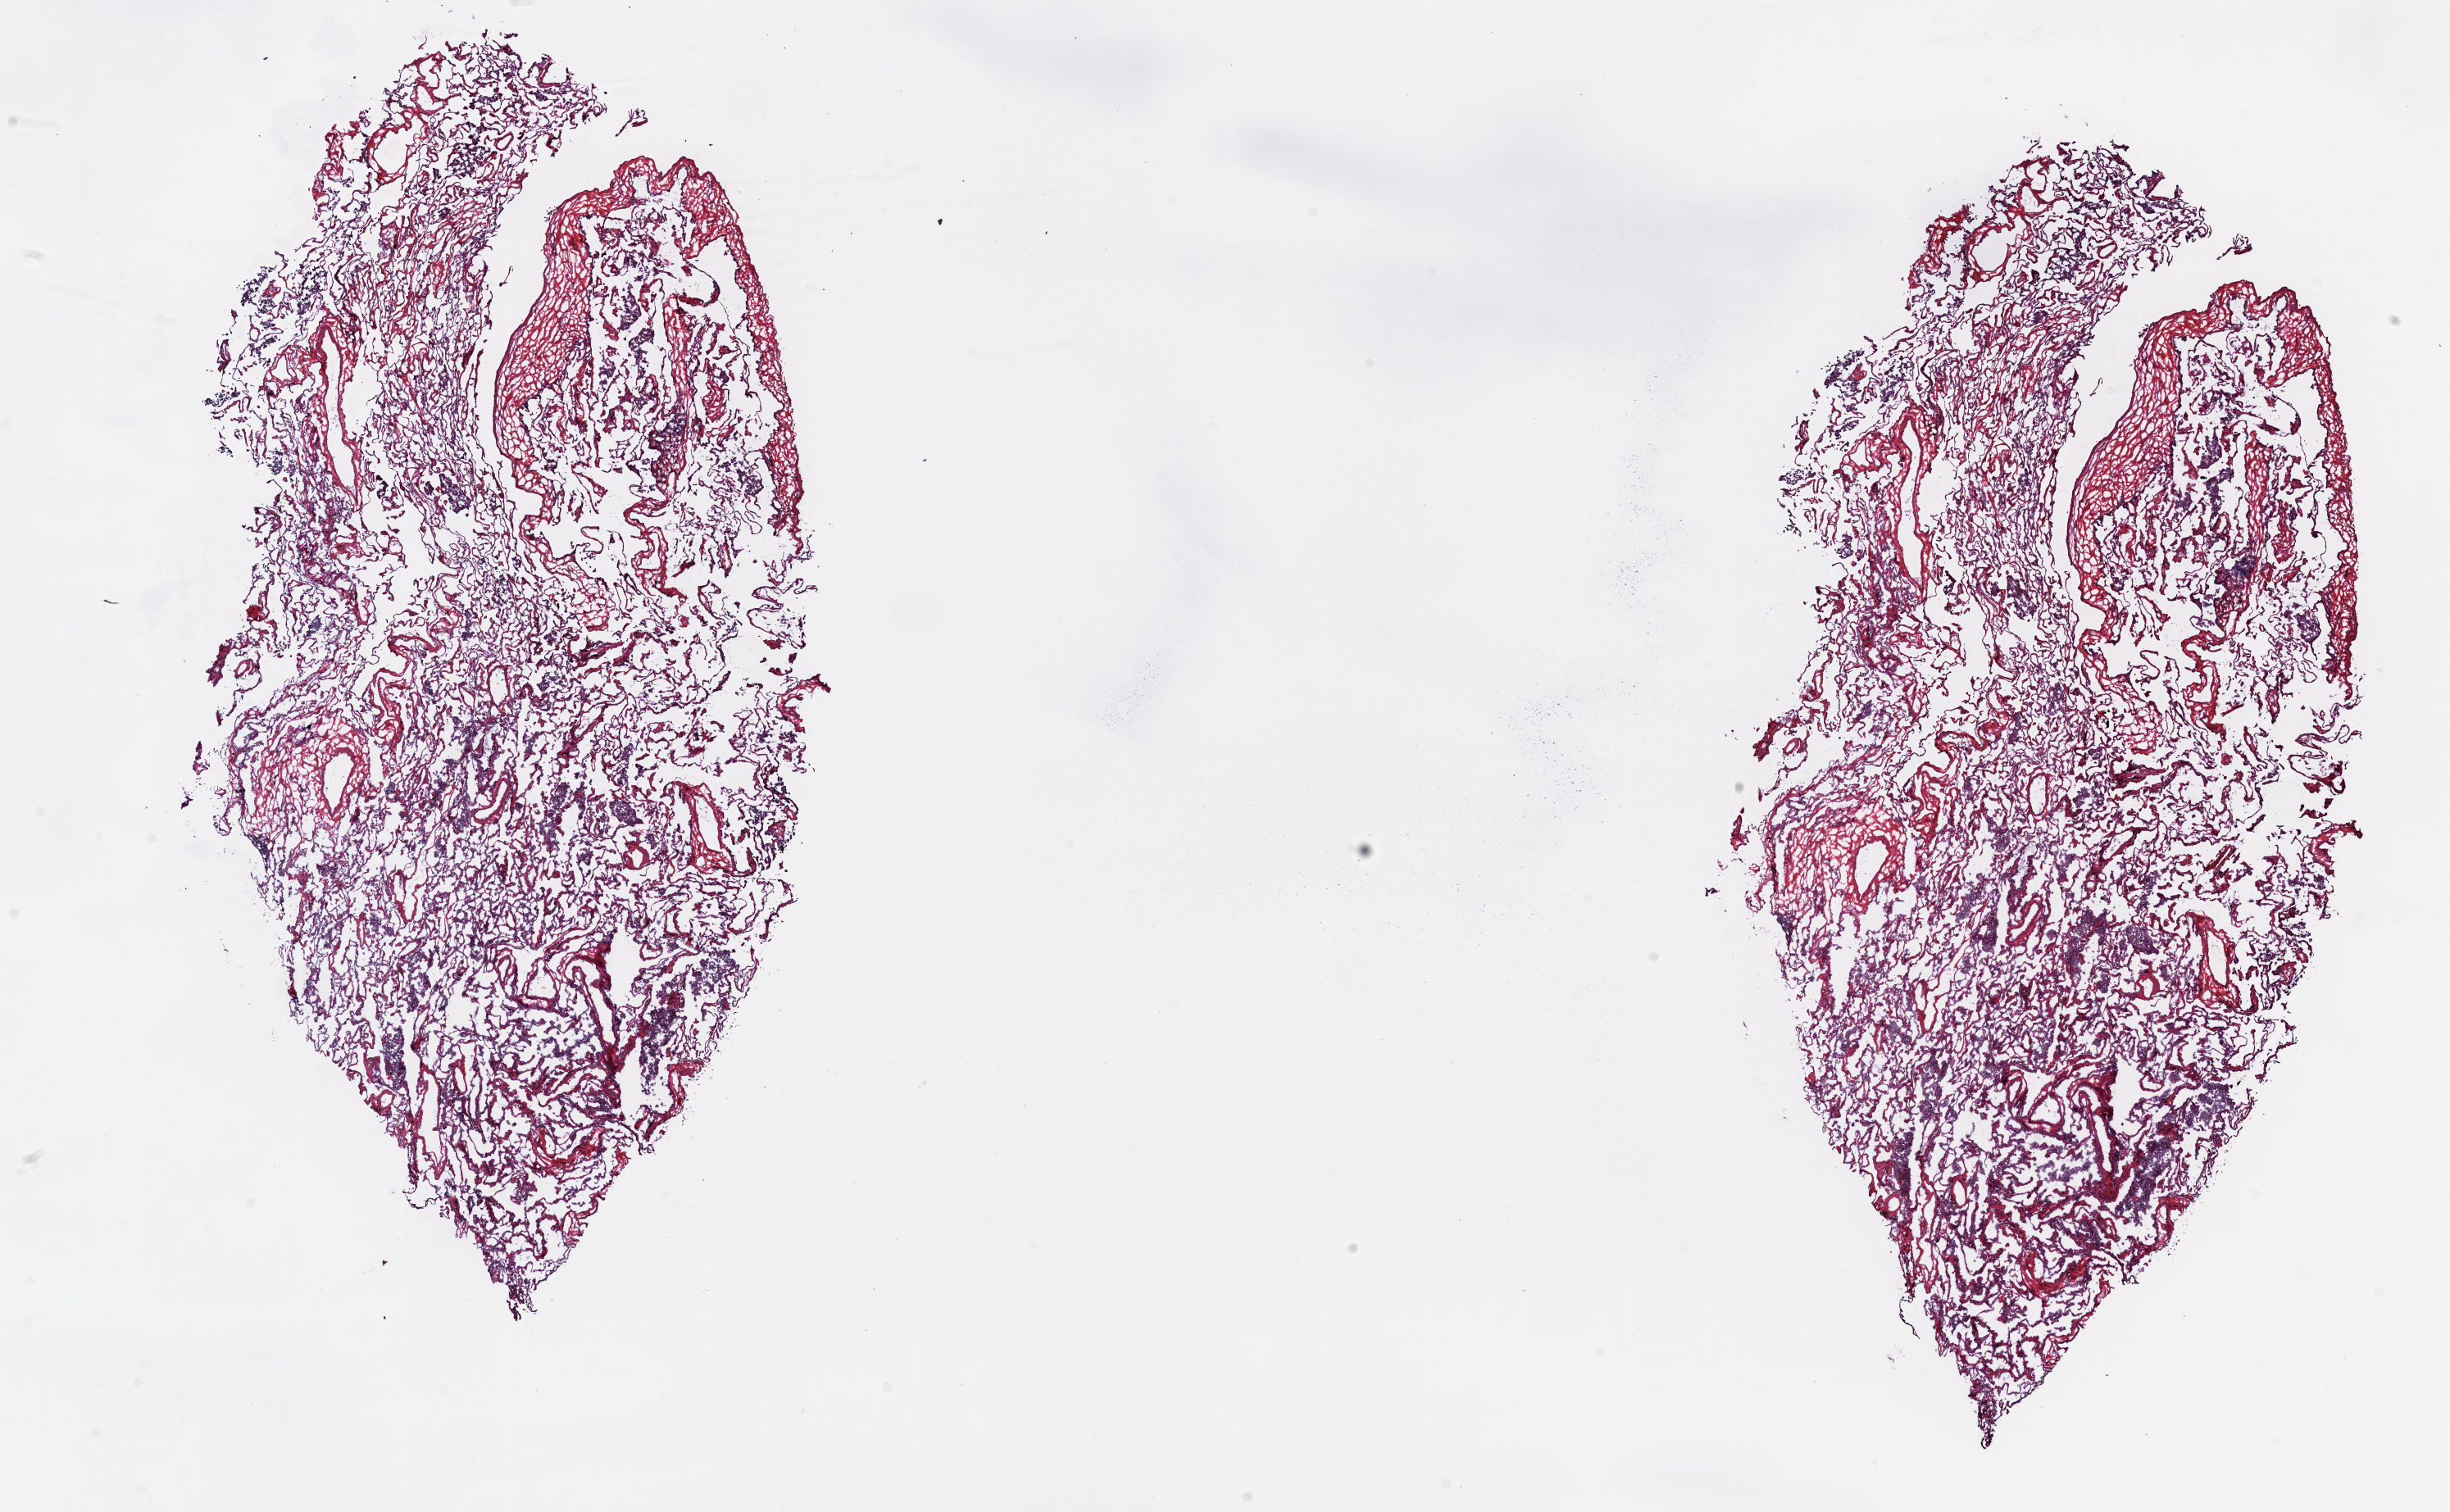
Whole-slide histology image, H&E-stained — whole scanned area (about 24.1 x 14.9 mm) shown as a low-resolution overview. Frozen section from the top of the tissue portion. Lung, solid tissue normal (non-tumour tissue) sample. Female, age 41 years at initial diagnosis. Pathologist review of this section (percent, as recorded): tumour cells 0%, tumour nuclei 0%, normal cells 50%, stromal cells 50%, necrosis 0%. Inflammatory infiltration, as recorded: lymphocyte infiltration 3%, monocyte infiltration 12%, neutrophil infiltration 3%.
- this section: solid tissue normal (non-tumour) sample from the same patient
- patient diagnosis: Adenocarcinoma, NOS